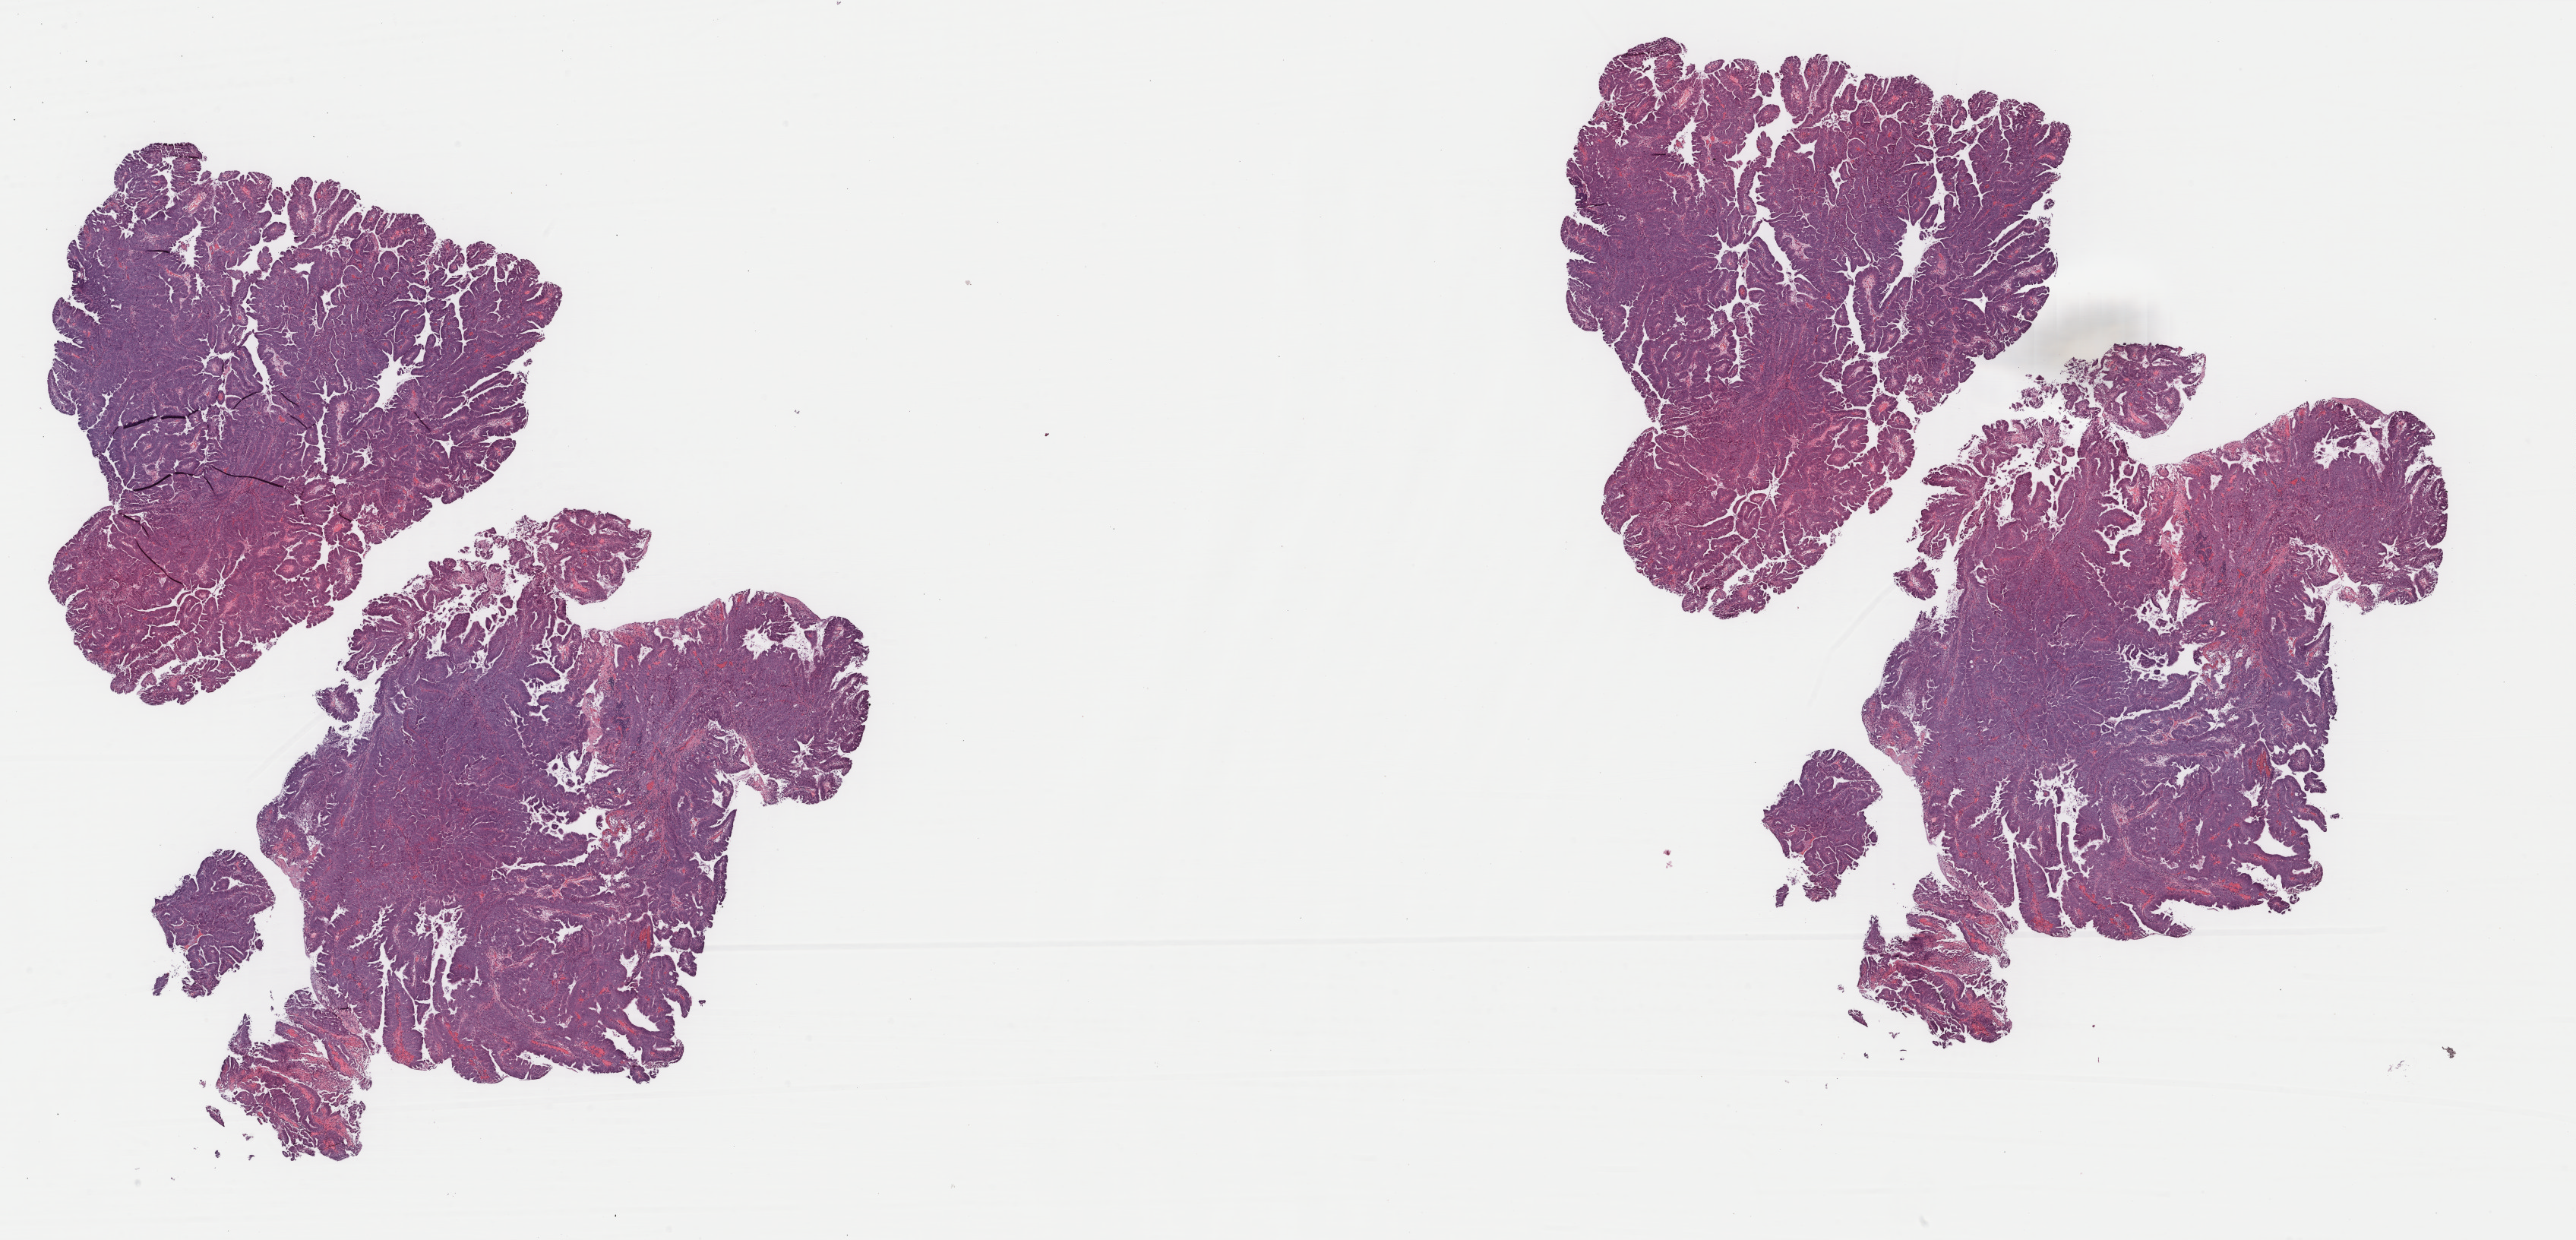
H&E whole-slide image — a low-resolution overview of the entire scanned area, about 26.9 x 13.0 mm (acquisition: 40x scan). FFPE section. Sample: primary tumour, stomach. Male, age 70 years at initial diagnosis. Histologic grade: G2 (moderately differentiated).
Lymph nodes positive (case pathology): 1 of 20 examined. TNM: T4b N1 MX. AJCC pathologic stage: IIIB (7th edition). Diagnosis: Adenocarcinoma, intestinal type (gastric antrum).